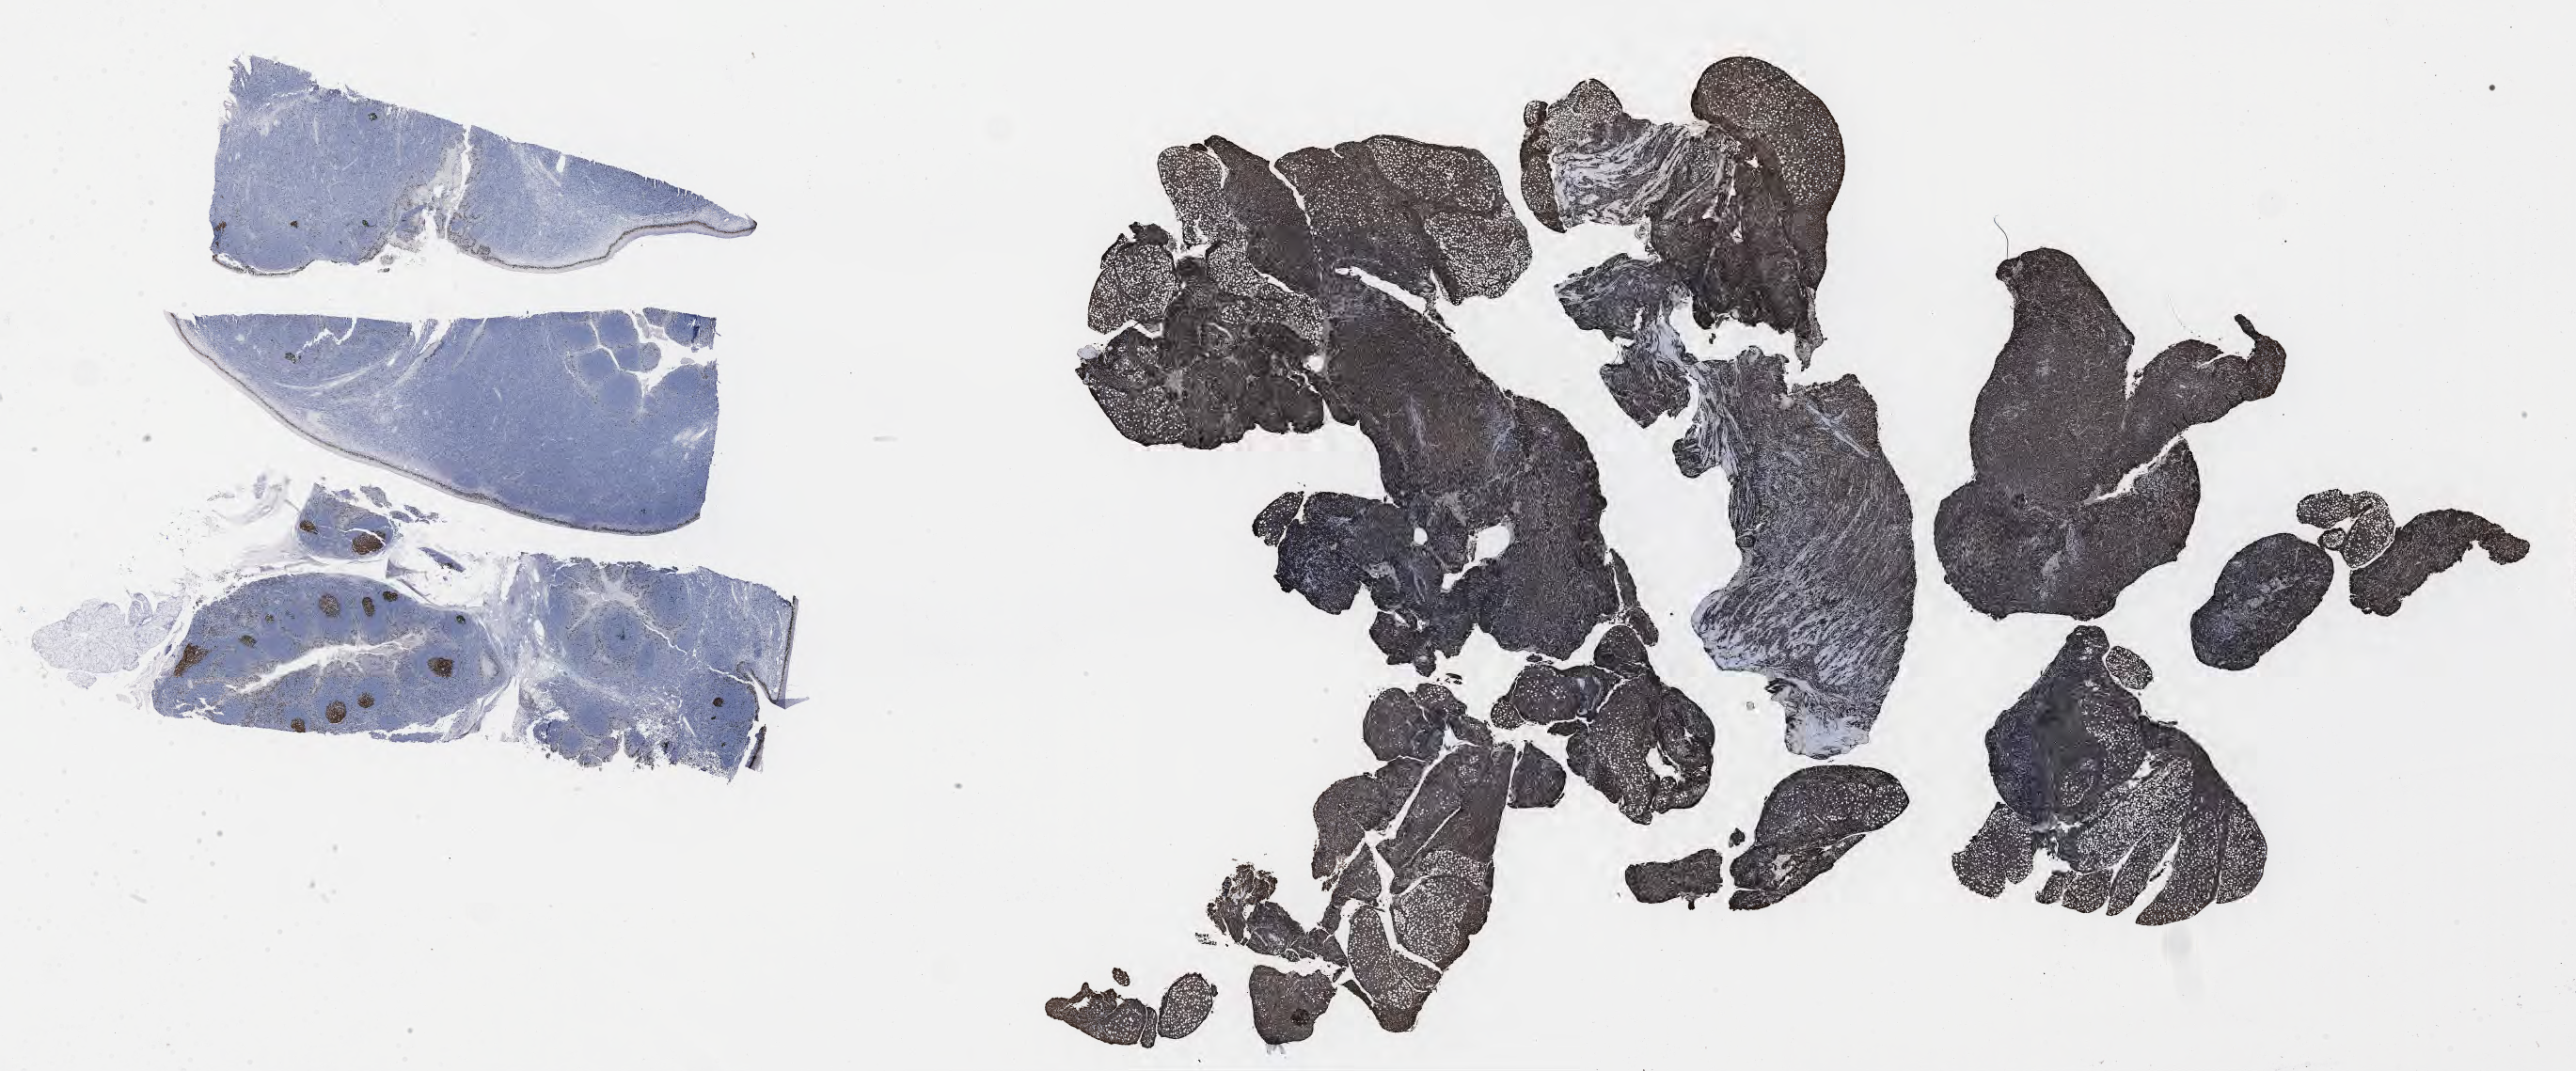
IHC for Ki-67, whole-slide image, shown as a low-resolution overview of the whole scanned area (about 44.3 x 18.4 mm), specimen: tumor tissue, site: abdomen proper. Male, age 4 years at initial diagnosis.
Diagnosis: Burkitt lymphoma, NOS.